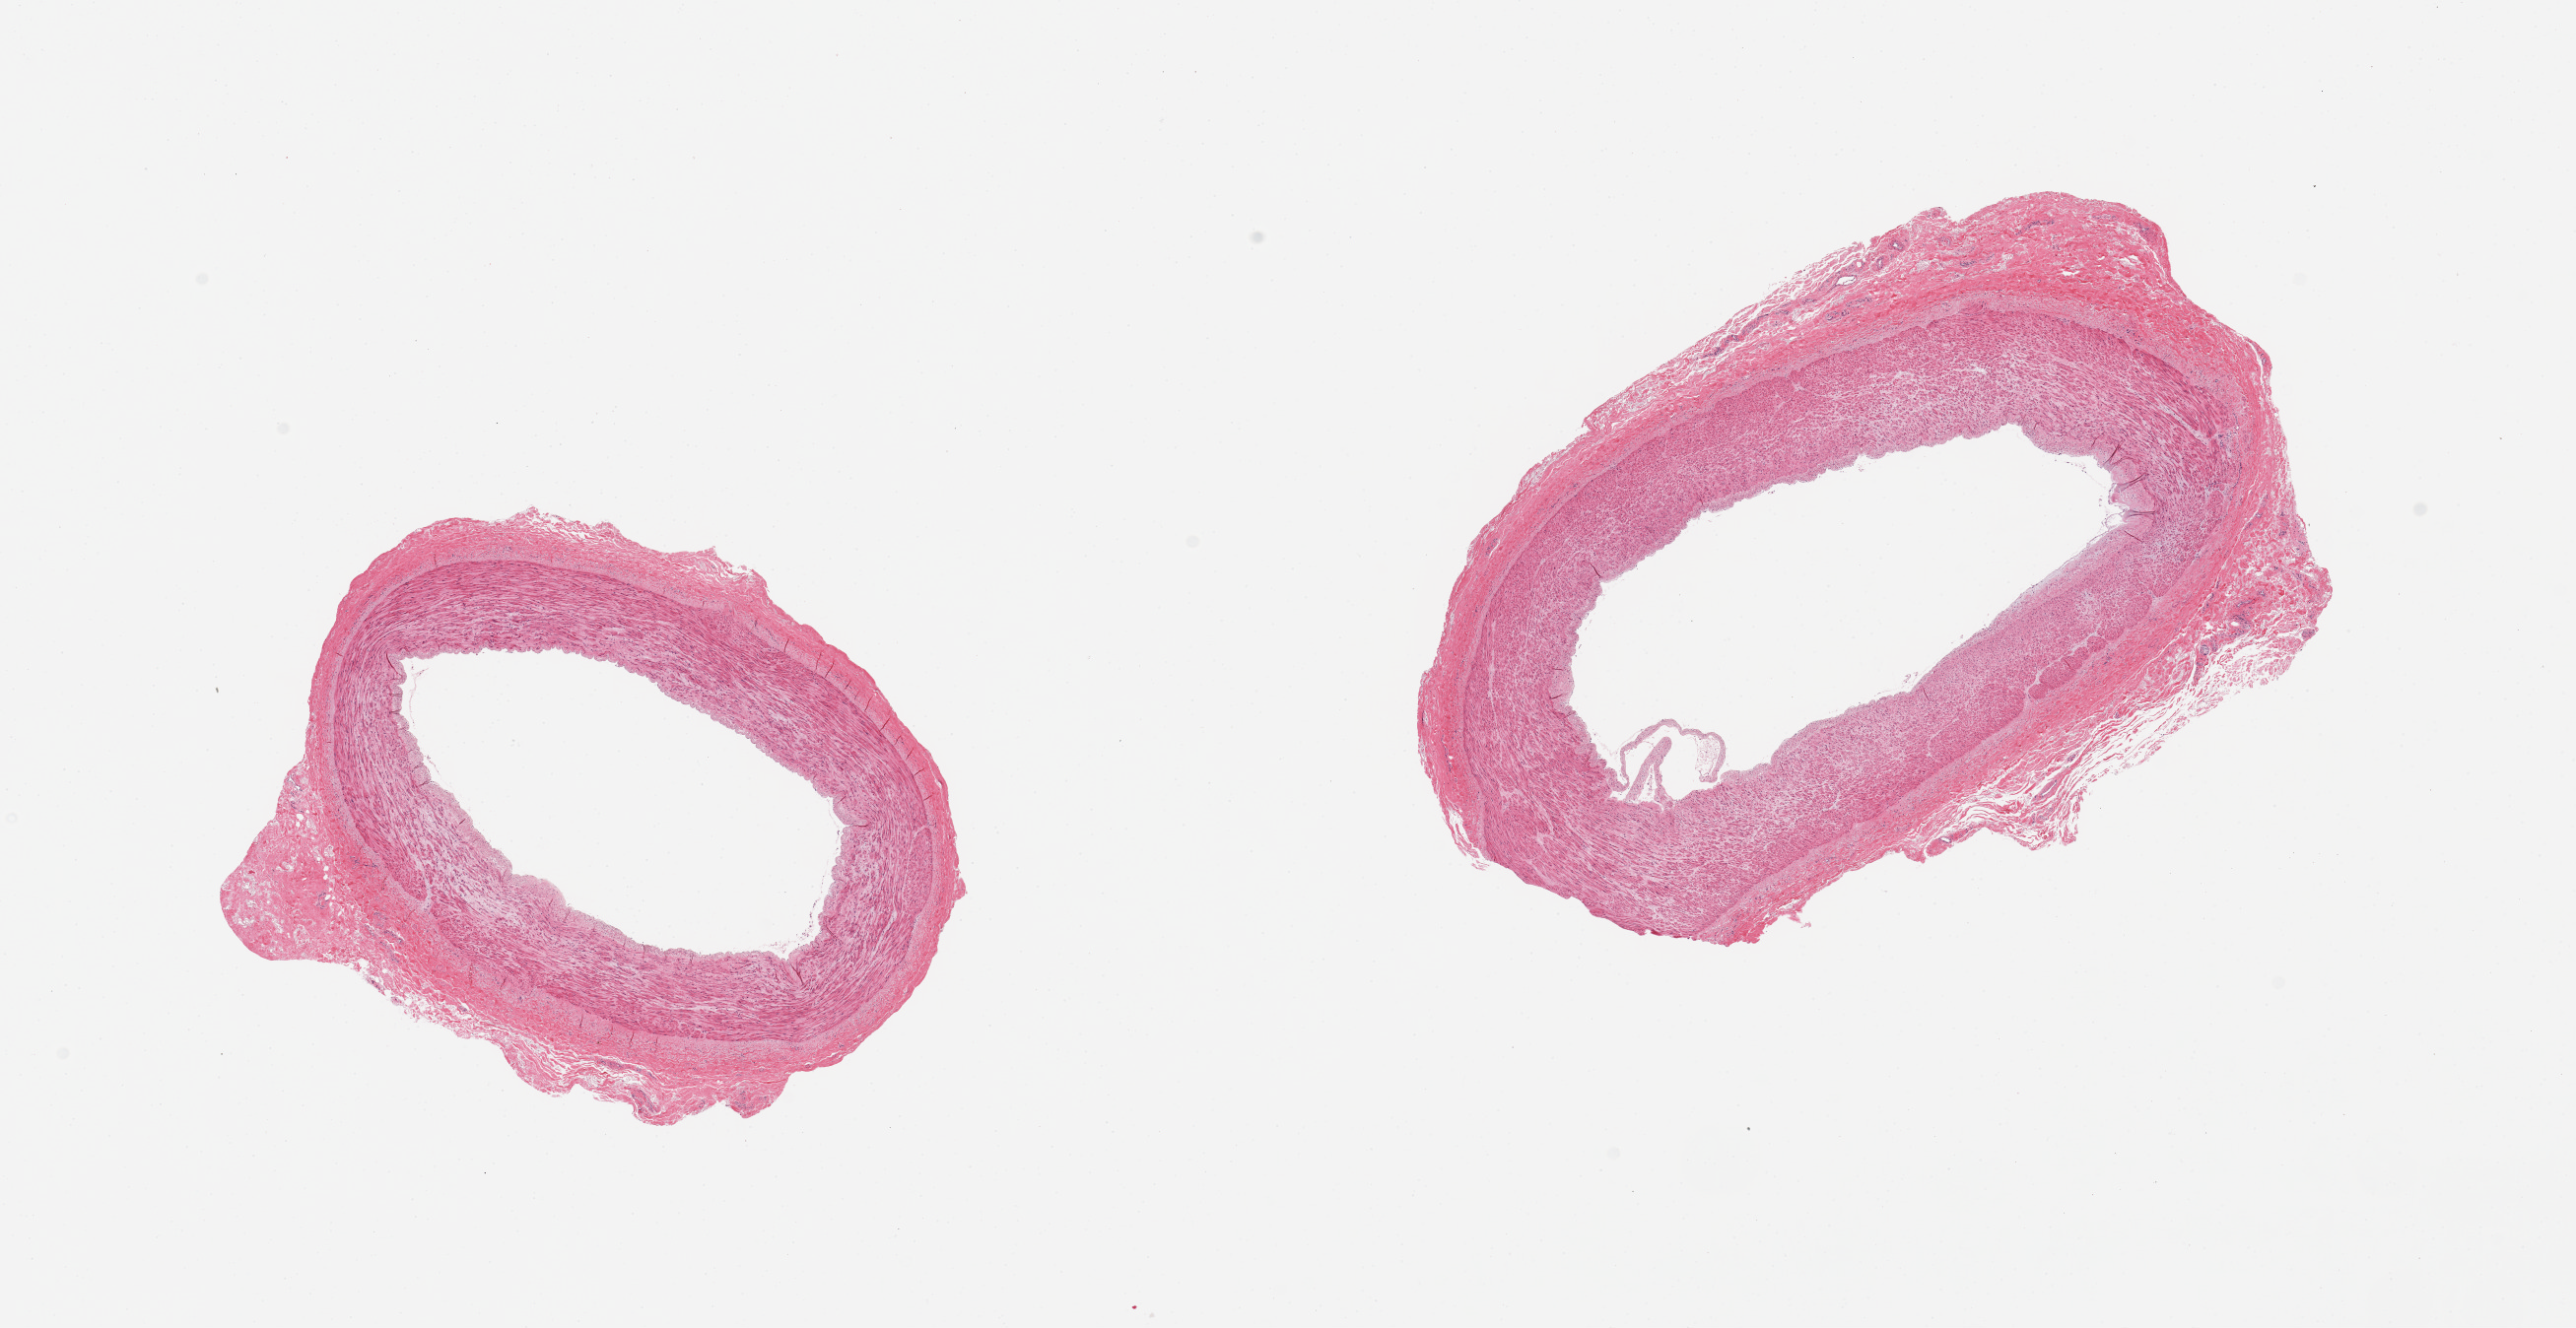
Whole-slide image, hematoxylin and eosin (H&E) stain, brightfield, a low-resolution overview of the entire scanned area, about 20.7 x 10.7 mm, PAXgene-fixed paraffin-embedded (PFPE) section, sampled site (target tissue): tibial artery, tissue donor sample. Donor: male.
• reviewer comment on this tissue sample: 2 pieces; intimal thickening and early atherosclerosis